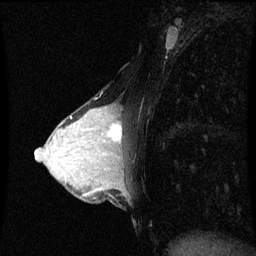
Breast MRI (dynamic contrast-enhanced), one sagittal slice. Slice 31 of 60 in the series (ordered by position). Dynamic contrast-enhanced series, image 2 of 3 at this slice position (ordered by acquisition). 1.5 T. TE 4.2 ms, TR 8.9 ms. 256 × 256 image matrix. Patient: female, 33 years. From the clinical record (not read from this slice): setting: breast cancer imaged before/during neoadjuvant chemotherapy; receptor status: HER2-positive.
Structures marked on this image (semi-automatic segmentation, software-assisted and operator-edited):
- analysis volume of interest (the breast-tissue region the enhancement analysis was run in; not a lesion): bounding box (x1, y1, x2, y2) in pixels: (95, 108, 124, 153)
- tumour enhancement mask (voxels above the 70 % enhancement threshold inside the analysis volume of interest): (108, 124, 122, 141)